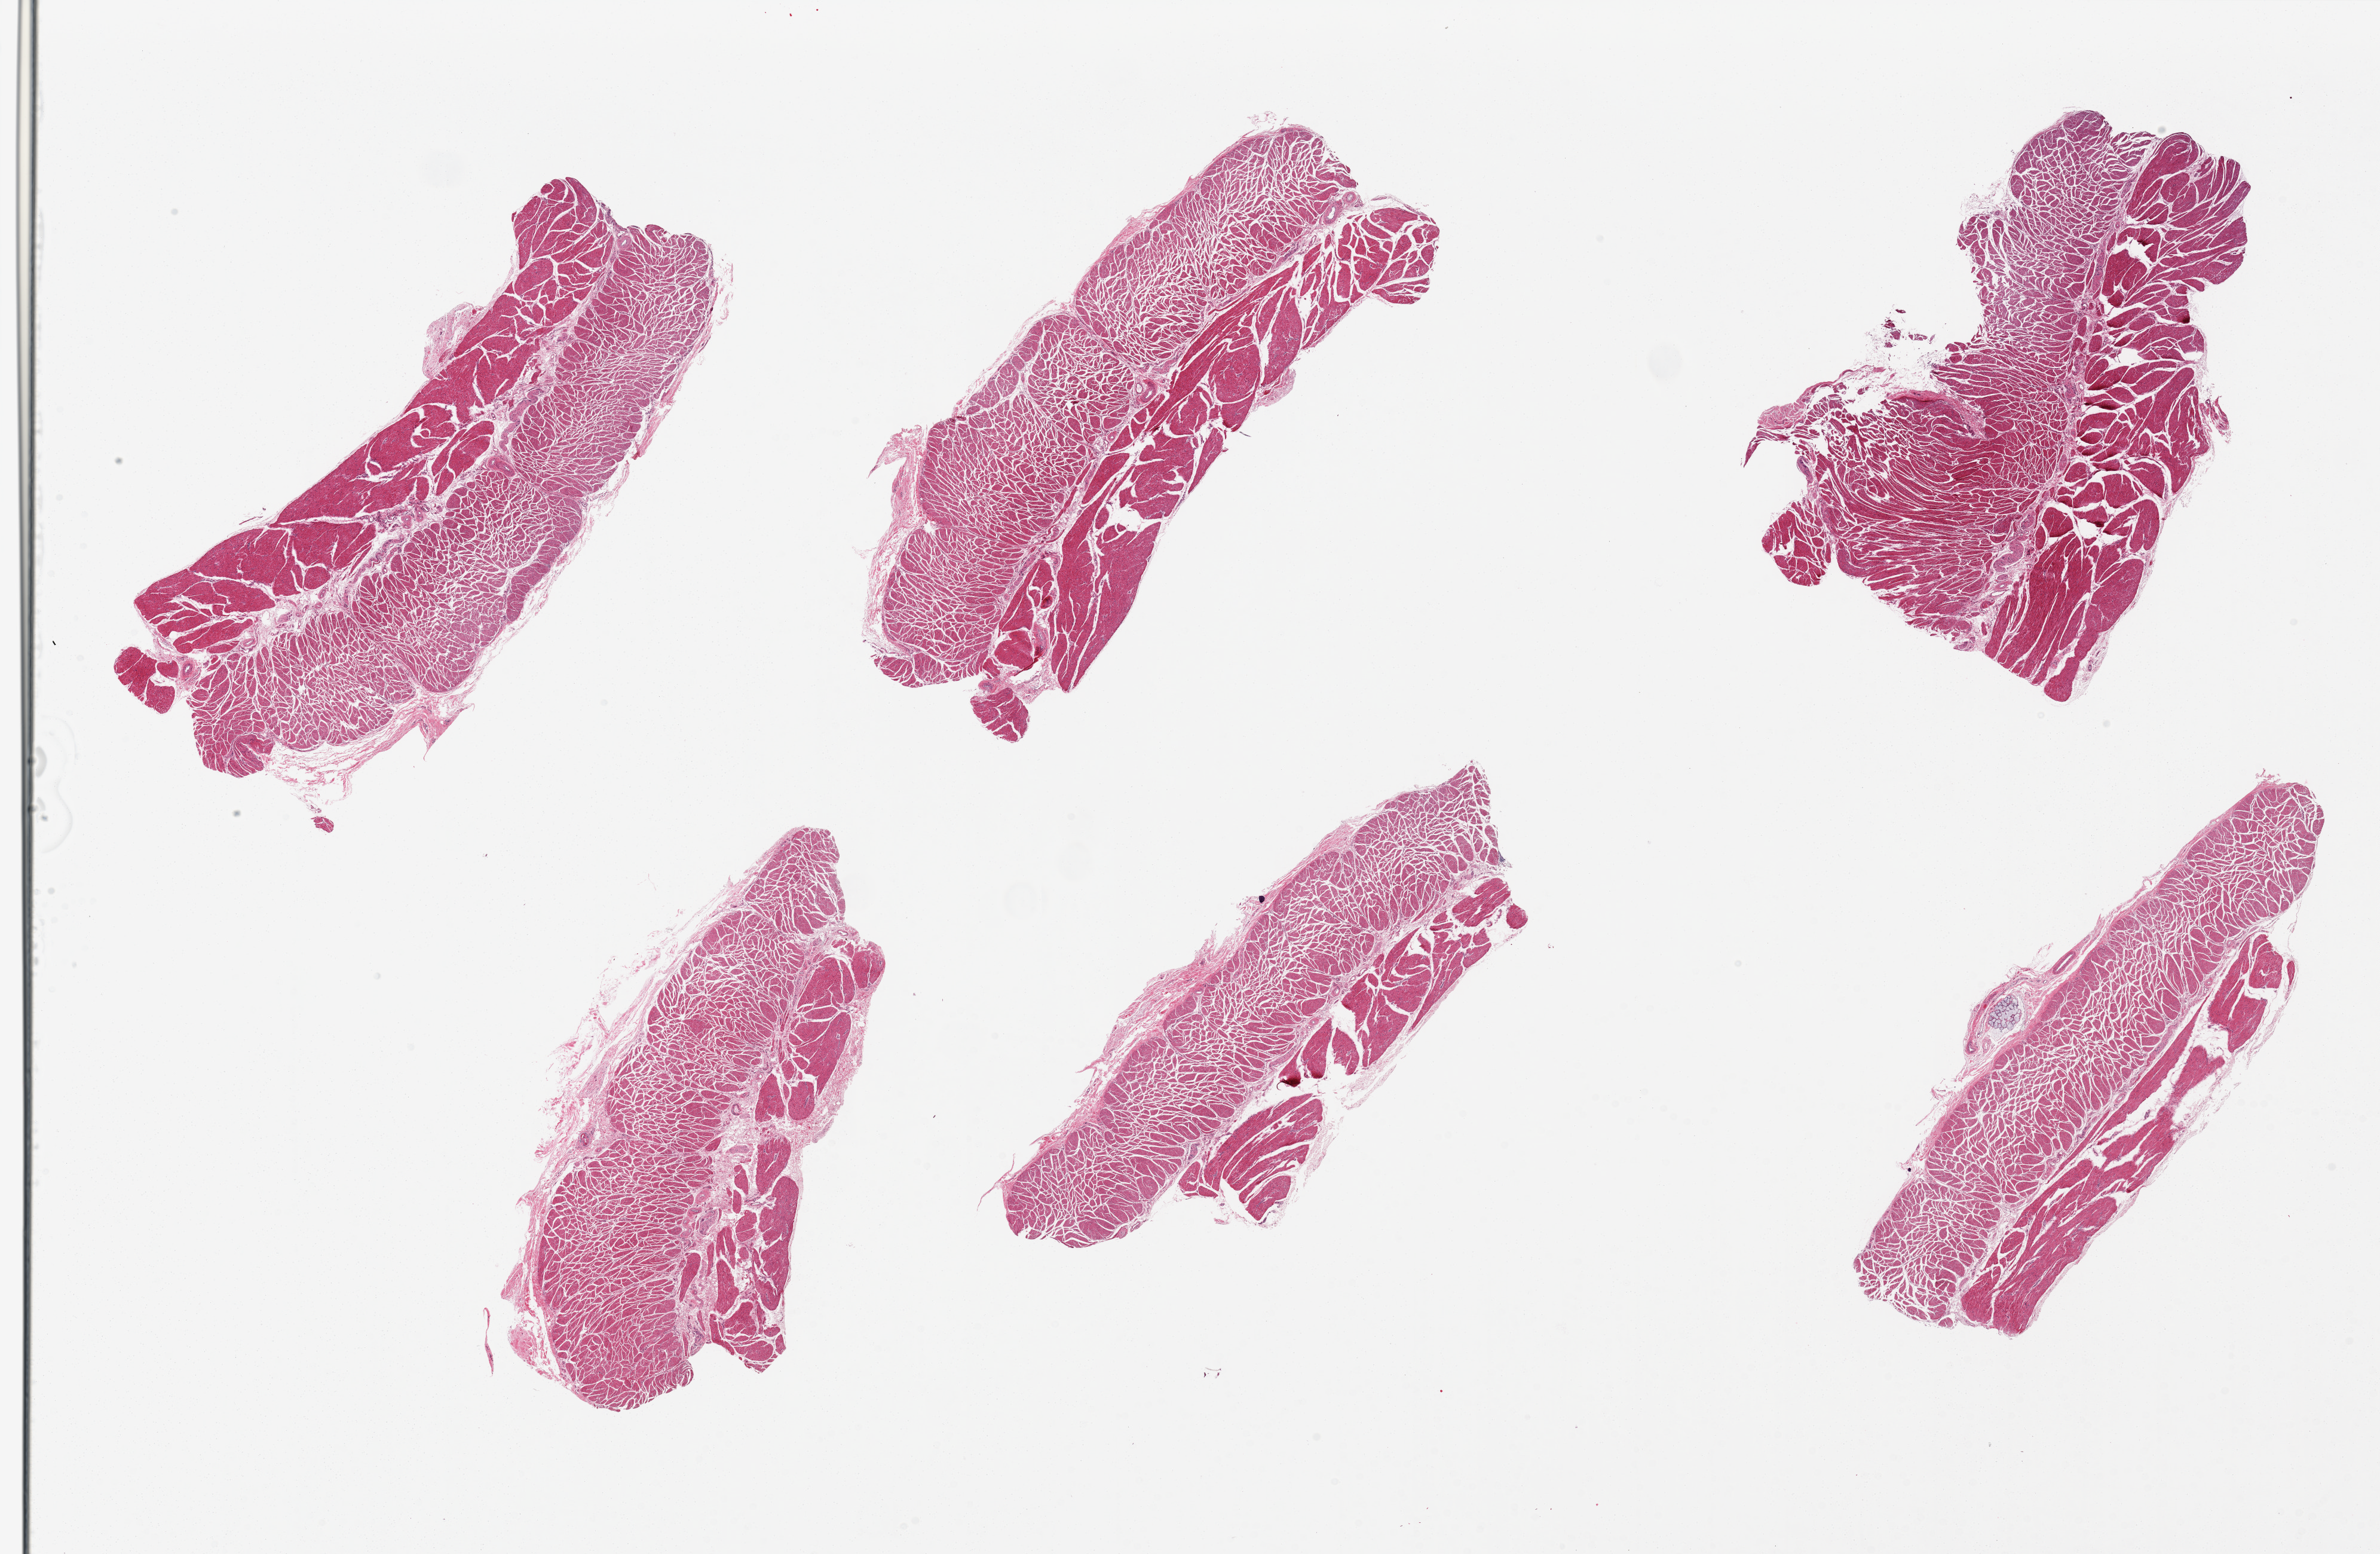
Digitized haematoxylin and eosin-stained section, brightfield — whole scanned area (about 31.5 x 20.6 mm, acquisition: 20x scan) shown as a low-resolution overview; PAXgene-fixed, paraffin-embedded tissue; section of esophageal muscle (target tissue); tissue donor sample. Donor sex: male.
Pathologist's review note for this sample: 6 pieces; relatively well-trimmed with small focus of mucous glands.